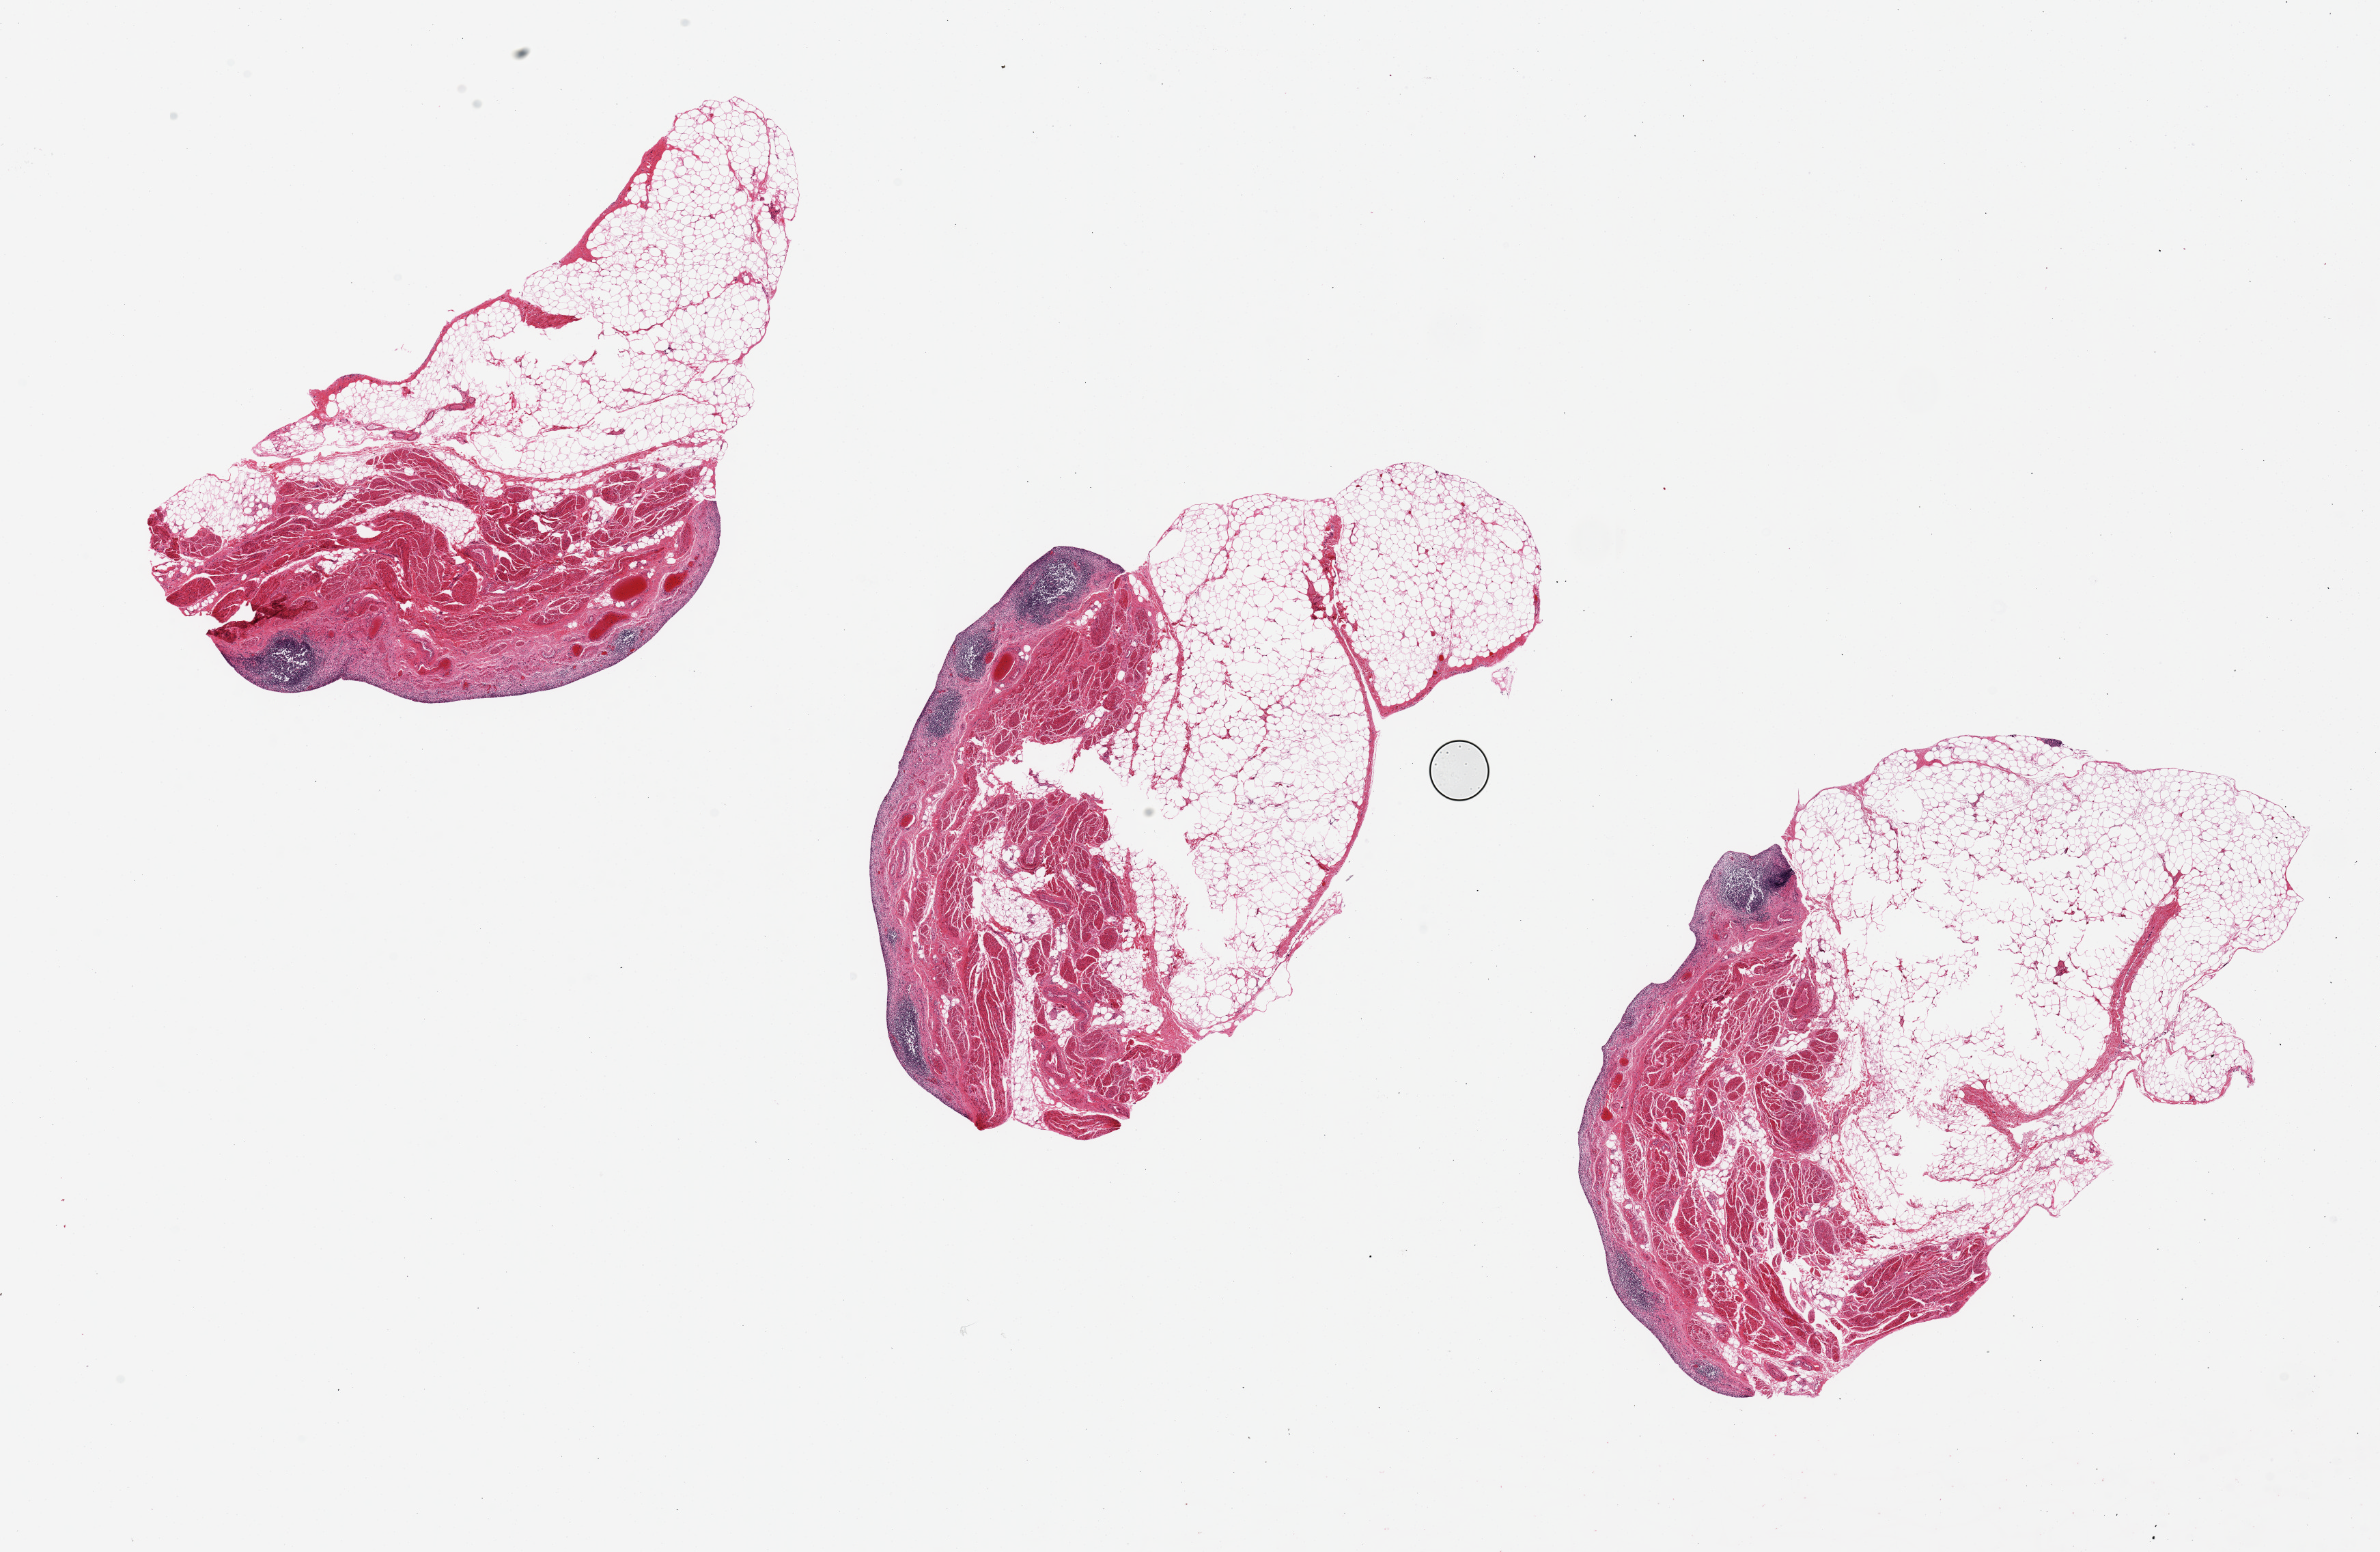
Whole-slide image, haematoxylin and eosin stain, brightfield, shown as a low-resolution overview of the whole scanned area (about 27.6 x 18.0 mm, slide scanned at 20x); PAXgene-fixed, paraffin-embedded tissue; section of urinary bladder (target tissue); donor tissue sample. Female donor.
• pathologist's review note for this sample: Mucosa completely autolyzed; marked diffuse lymphocytic cystitis